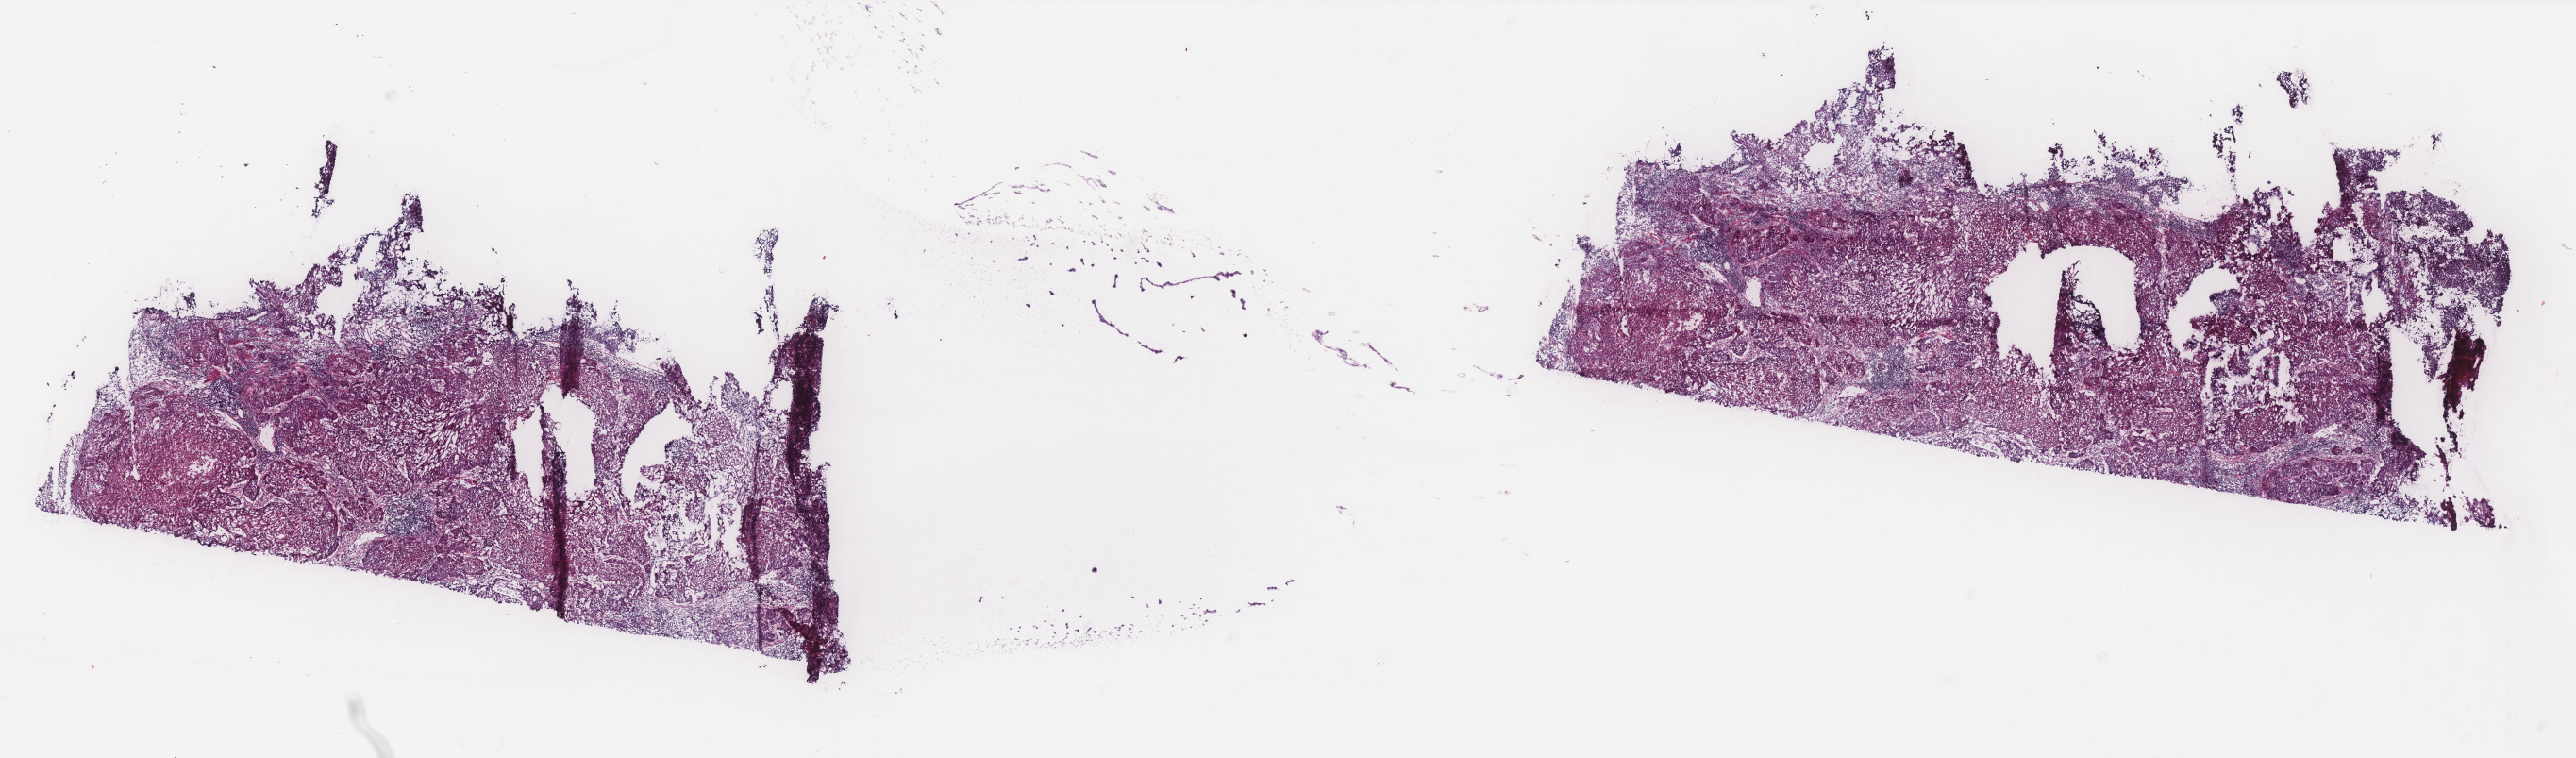
Hematoxylin and eosin (H&E) stained whole-slide image — shown as a low-resolution overview of the whole scanned area (about 21.9 x 6.4 mm, from a 40x scan); frozen section; primary tumour sample from the bladder. Female, age 70 years at initial diagnosis. Histologic grade: high grade. Slide review estimates, as recorded: tumour cells 60%, tumour nuclei 70%, normal cells 0%, stromal cells 30%, necrosis 10%. Infiltration values recorded for this section: lymphocyte infiltration 10%, monocyte infiltration 0%, neutrophil infiltration 5%.
Lymph nodes positive (case pathology): 0 of 14 examined. AJCC pathologic stage: III (6th edition). Histologic diagnosis: Transitional cell carcinoma.